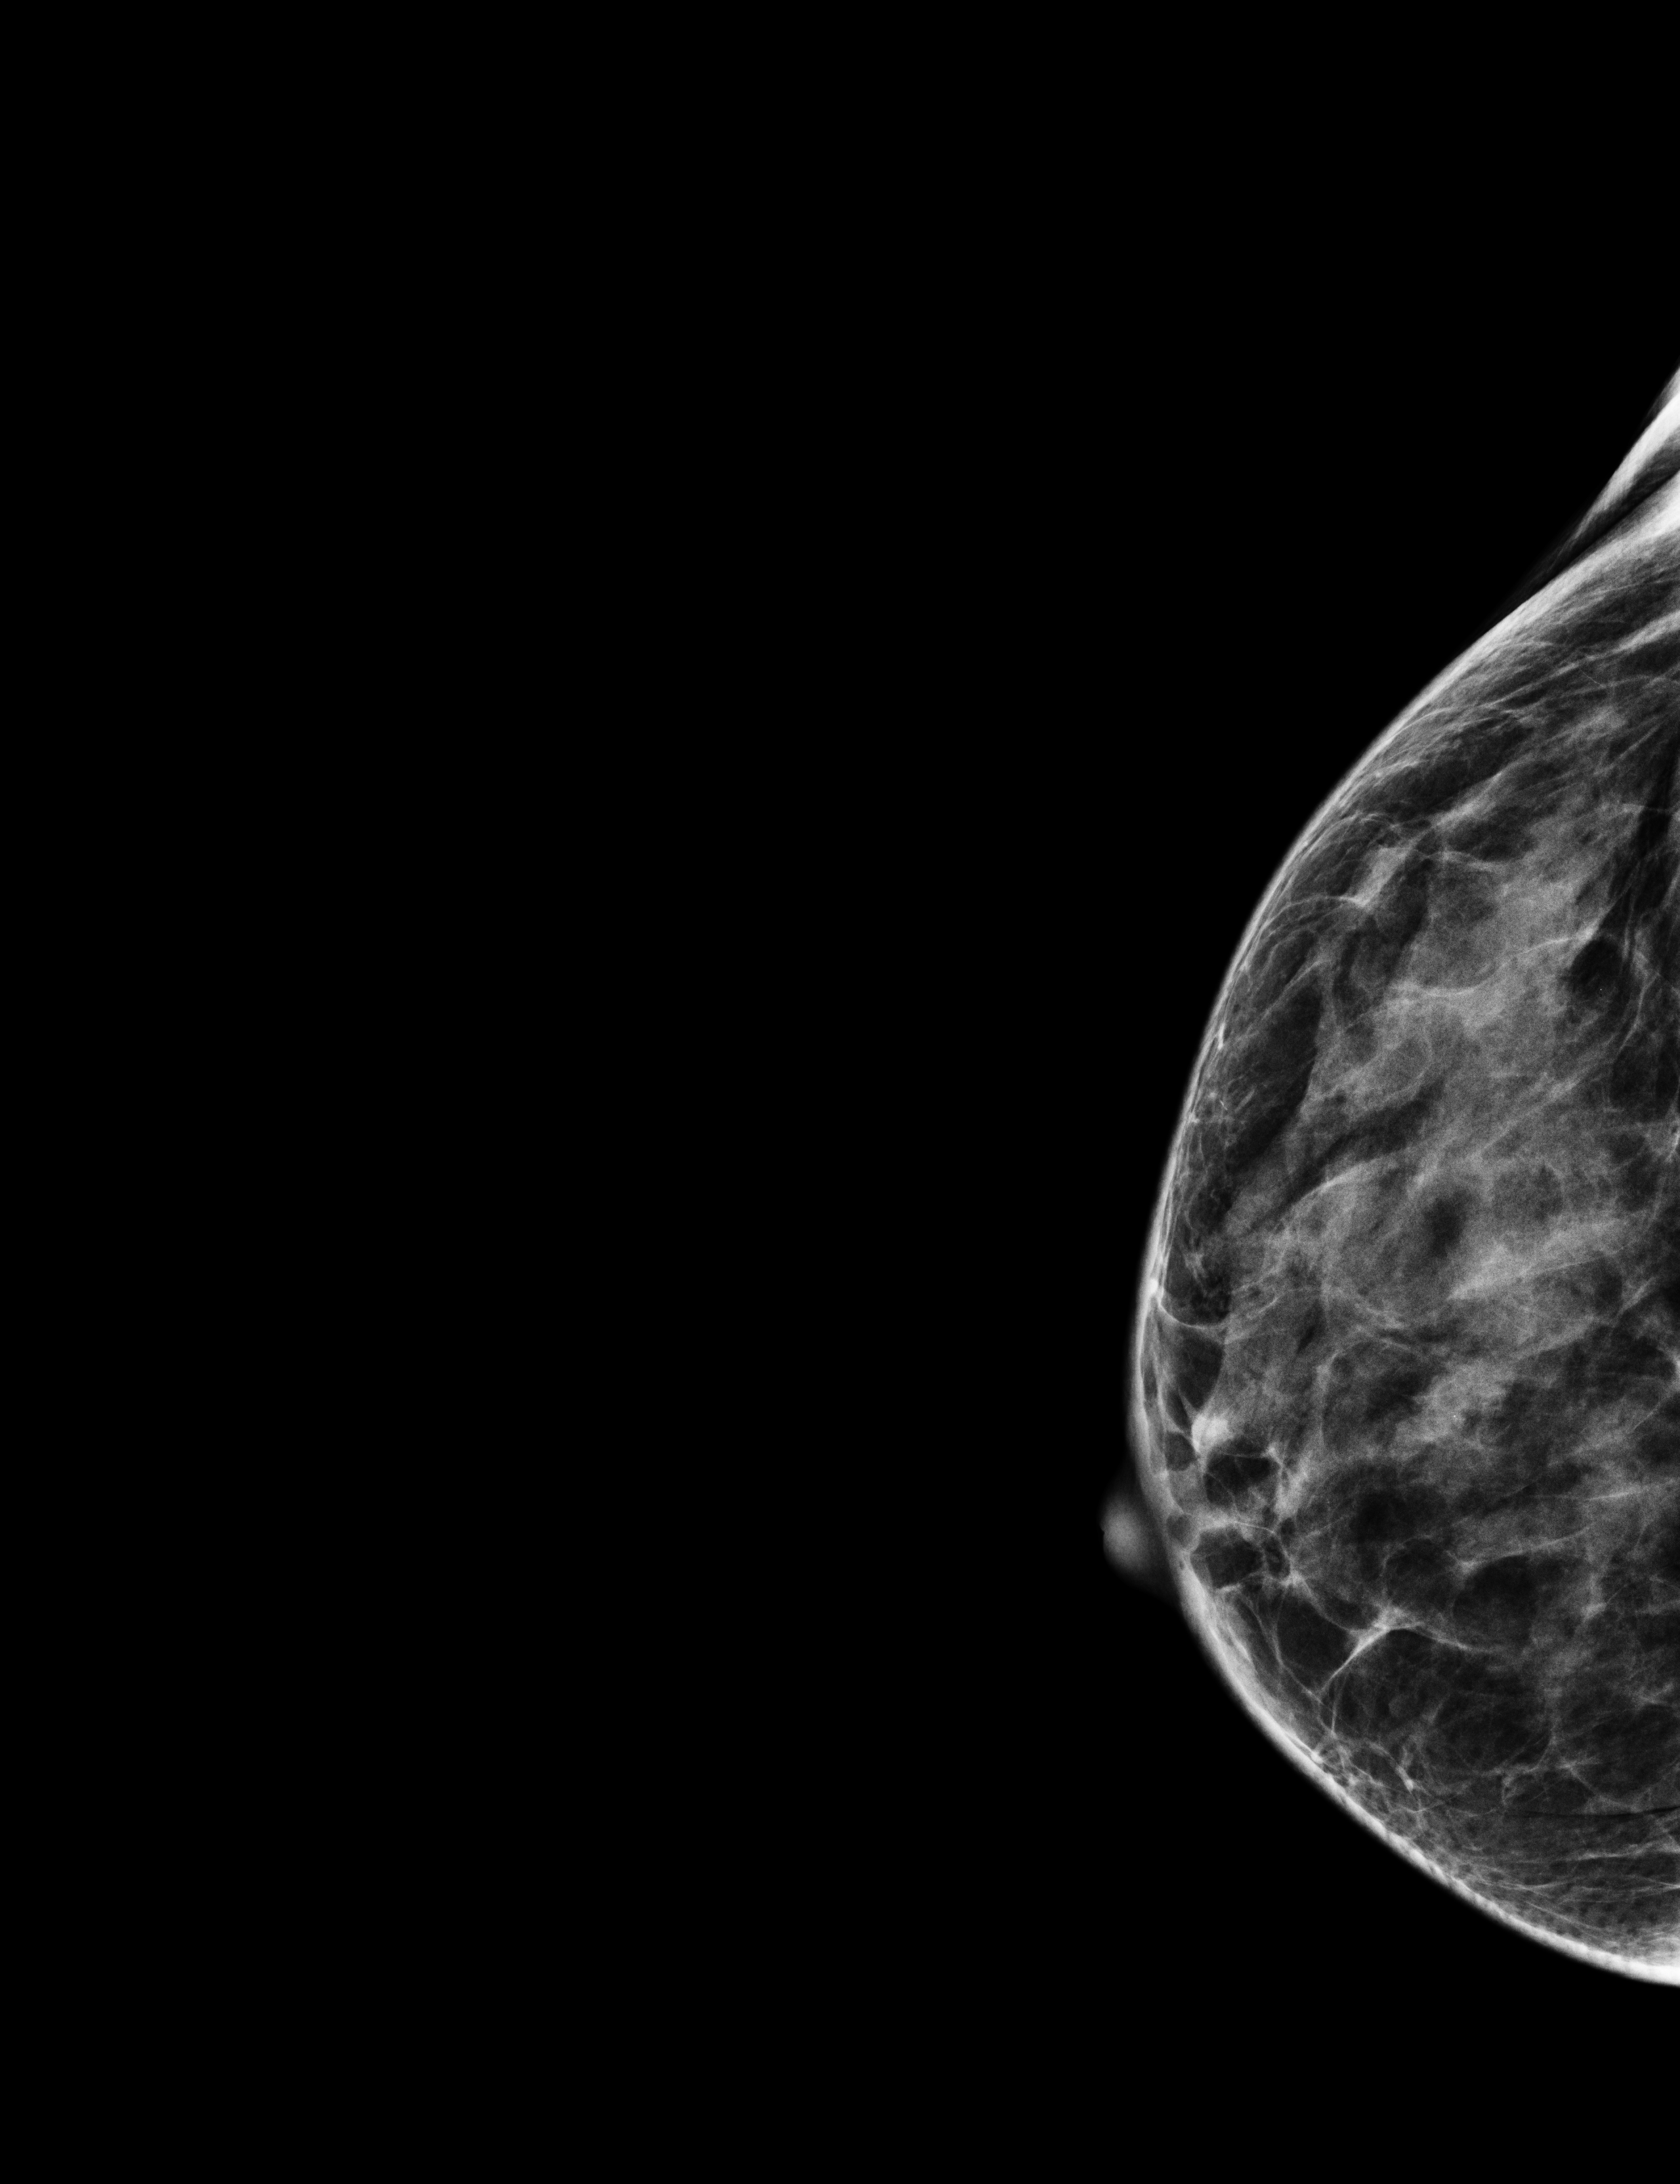
Full-field digital mammogram (FFDM); right breast; laterally exaggerated craniocaudal (XCCL) view; annual screening mammography examination; system: Selenia Dimensions. Patient: female, 52 years.
Breast density at the screening exam (both breasts): heterogeneously dense (BI-RADS density category c). Final BI-RADS assessment for this screening round (tomosynthesis exam, both breasts): category 1. Recall: no recall after this screen.